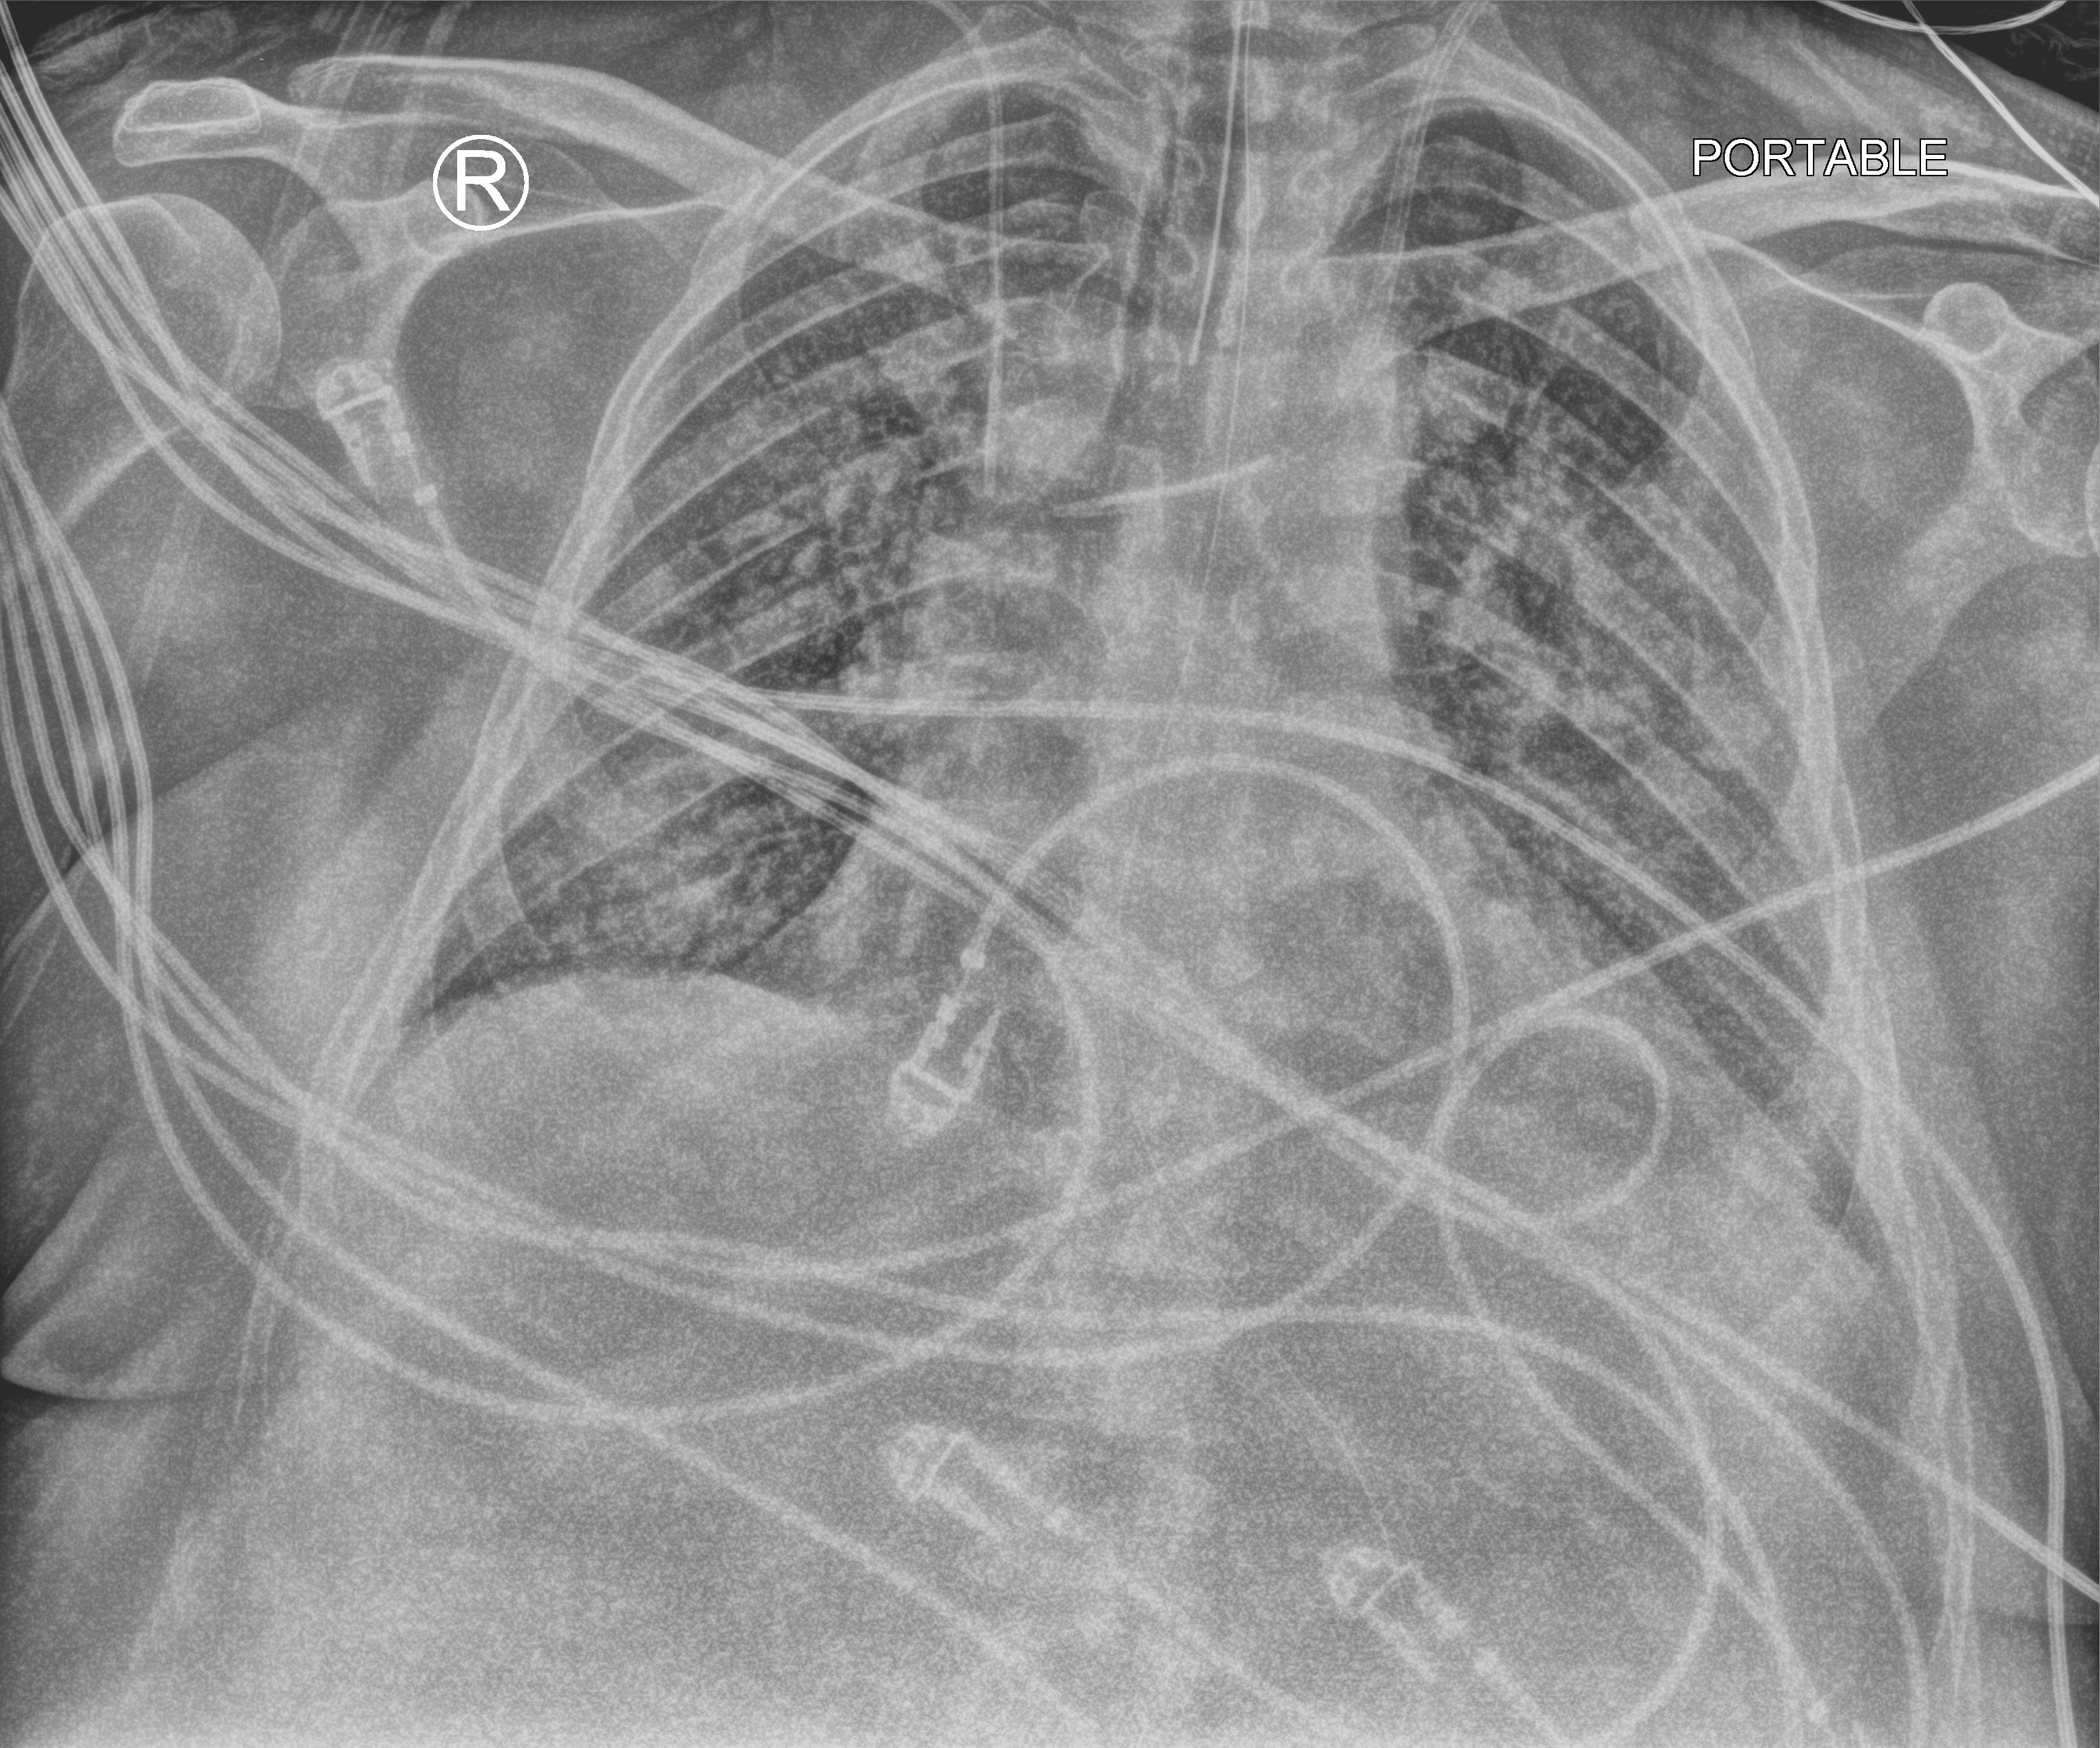
Bedside chest radiograph (computed radiography), anteroposterior (AP) projection. Male patient hospitalised with COVID-19, age 18–59 years.
Hospital-stay facts (about this admission, not read from this image; timing relative to this image not recorded): mechanically ventilated during this hospital stay: yes; admitted to intensive care during this hospital stay: yes; chronic kidney disease (admission record): no.